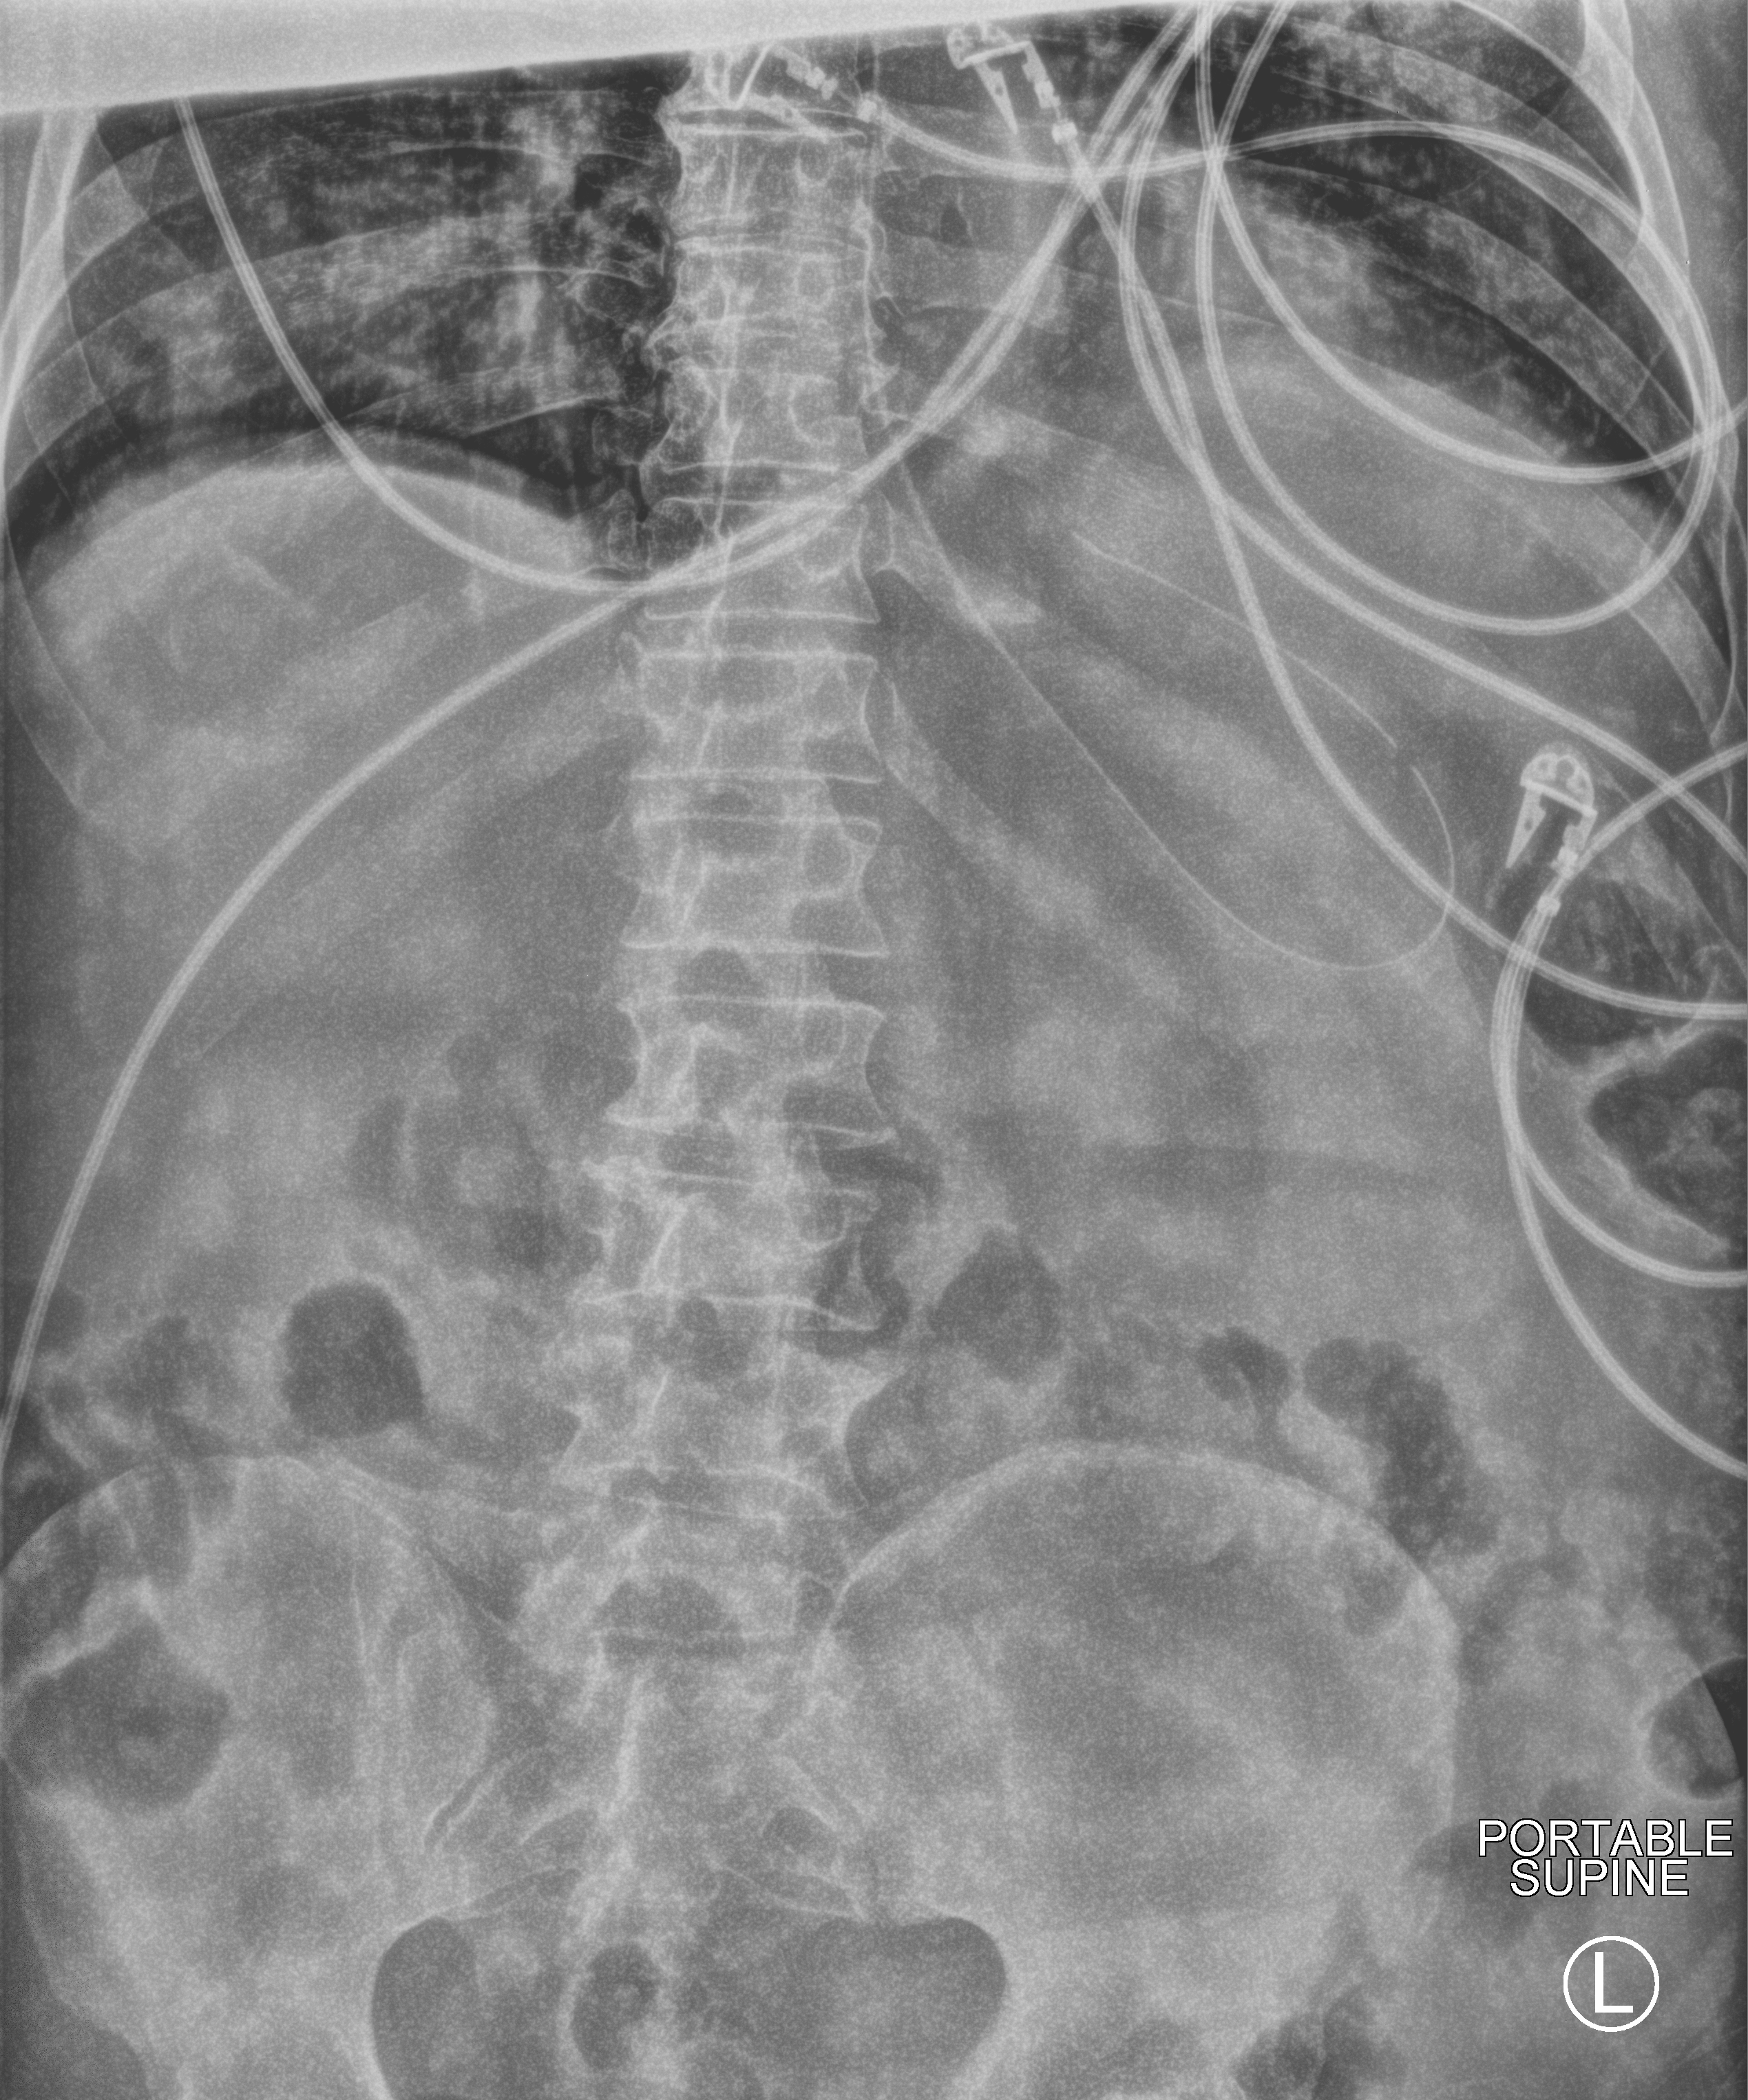
Portable abdomen radiograph; anteroposterior (AP) projection. Patient hospitalised with COVID-19; male, aged 60–74 years.
Admission-level facts for this patient (not findings on this image; timing relative to this image not recorded): admitted to intensive care during this hospital stay: yes; hypertension (admission record): yes.